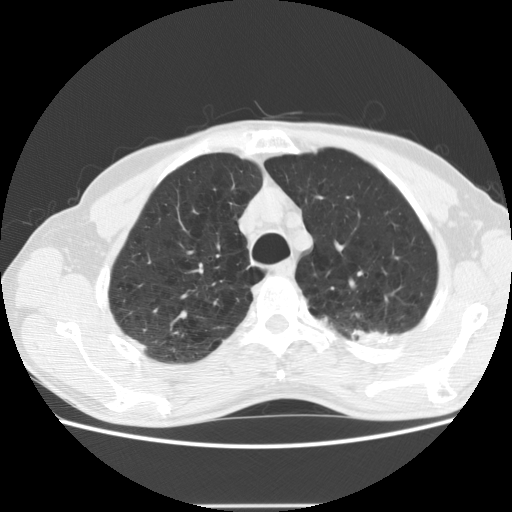
Low-dose screening chest CT, one axial slice; slice 155 of 191 in the series (ordered by position); reconstruction kernel STANDARD; 120 kVp; lung window (W 1500 / L -600 HU); 512 × 512 image matrix.
Annotated regions visible in this slice (expert manual segmentation):
- lesion 1 (tumor, upper lobe of left lung): bounding box <352,330,388,342> (left, top, right, bottom; pixels)